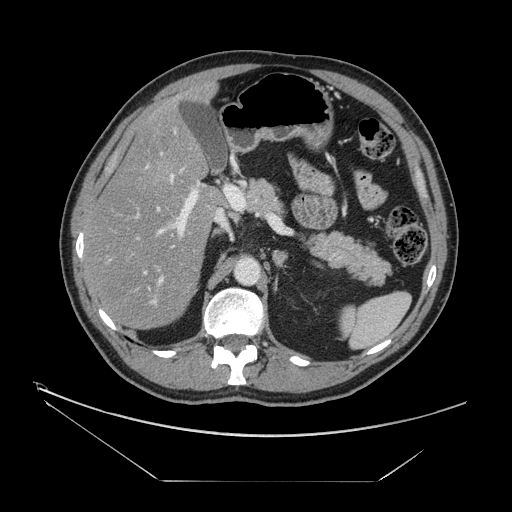
Contrast-enhanced abdominal CT, one axial slice; slice 84 of 161 in the series (ordered by position); intravenous contrast given; soft-tissue window (W 400 / L 40 HU); 2.5 mm slice thickness; 512 × 512 image matrix, field of view 440 × 440 mm. Male patient, age 65 years. From the clinical record (not read from this slice): diagnosis: colorectal cancer liver metastases, imaged before liver resection; multiple liver metastases: yes; largest metastasis: 4.2 cm; disease in both lobes: yes.
Structures marked on this image (manually delineated by an expert):
- hepatic veins: bounding box <136,168,185,291> (left, top, right, bottom; pixels)
- liver: <85,86,222,329>
- planned liver remnant (the part of the liver to remain after resection): <95,87,220,329>
- portal vein (with intrahepatic branches): <112,152,218,307>